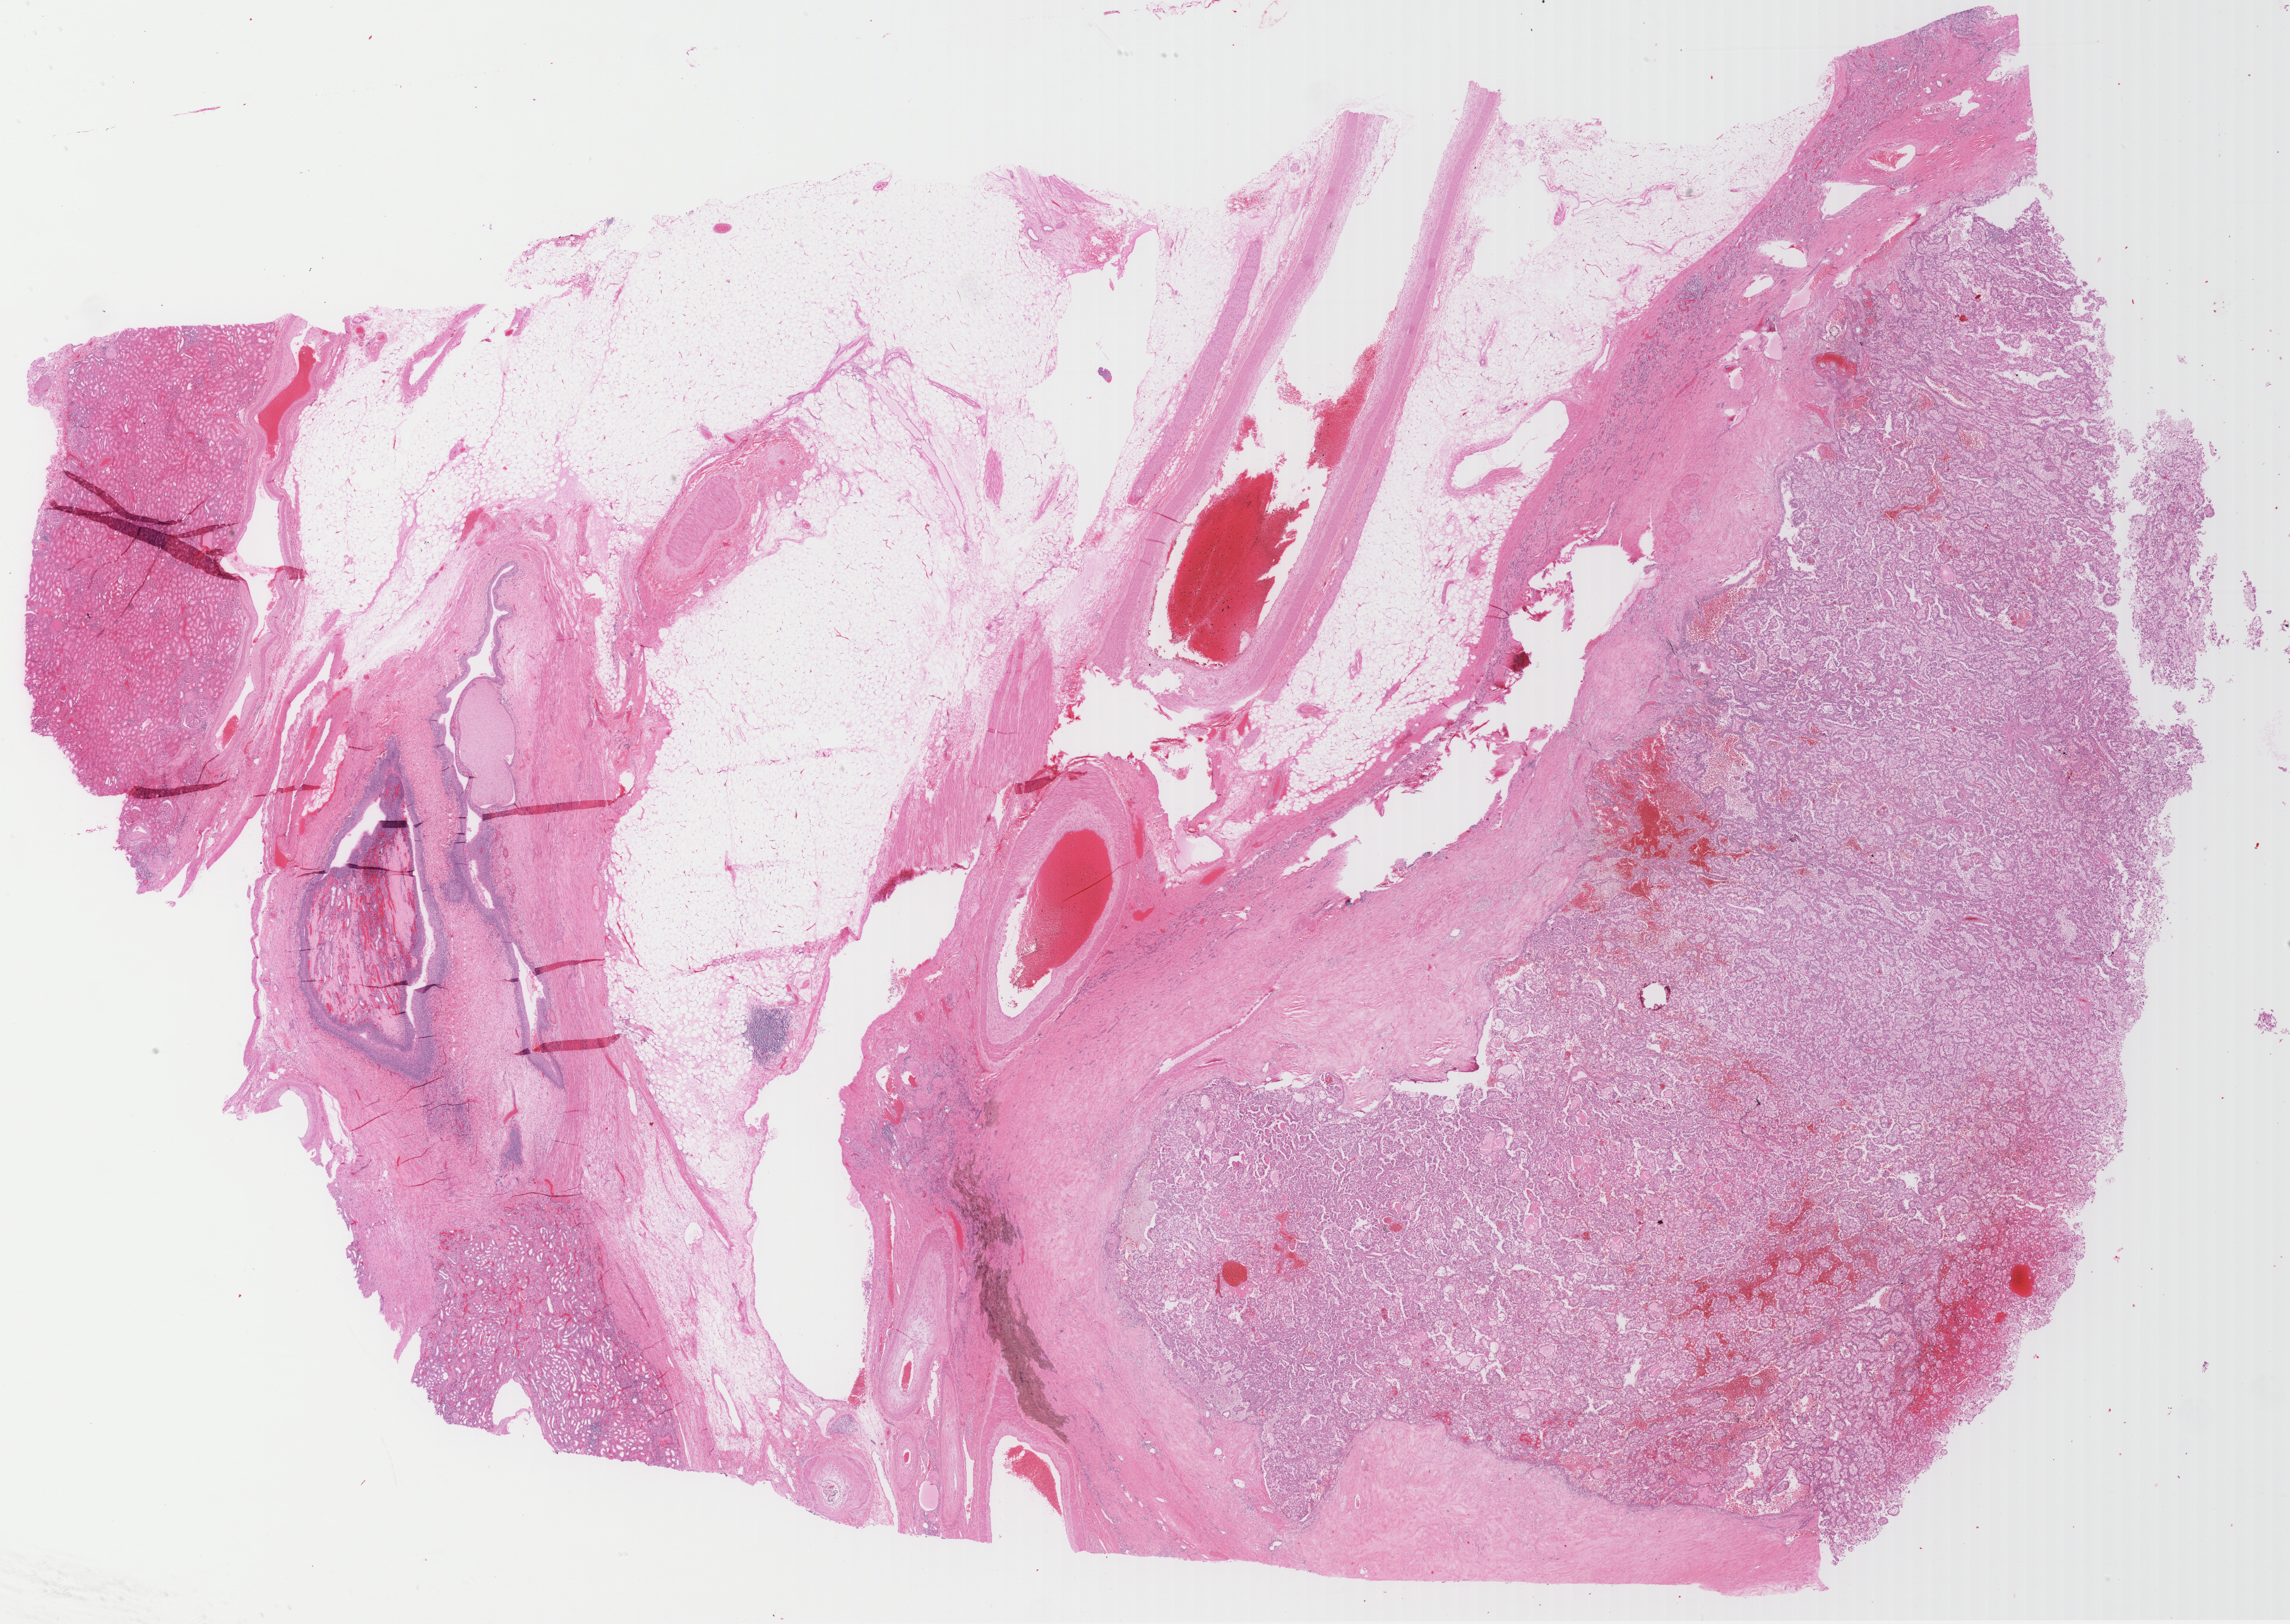
Hematoxylin and eosin (H&E) stained whole-slide image — whole scanned area (about 29.4 x 20.9 mm, from a 40x scan) shown as a low-resolution overview, formalin-fixed paraffin-embedded (FFPE) diagnostic section, kidney, primary tumour sample. Male patient; age at initial diagnosis 67 years.
- histologic diagnosis: Papillary adenocarcinoma, NOS
- AJCC pathologic stage: II (6th edition)